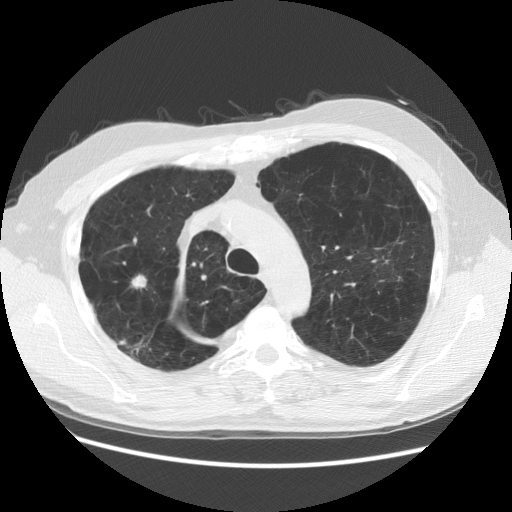
Low-dose screening chest CT, axial slice. Third annual screen. Lung window (W 1500 / L -600 HU). Slice 103 of 137 in the series. 512 × 512 image matrix. Male, age 58 years at enrolment. Former smoker at enrolment.
Expert-annotated lung lesion, bounding box [x1, y1, x2, y2] px = [113, 258, 159, 306]. The screening reader recorded 3 non-calcified nodules or masses ≥4 mm on this exam (right lower lobe, right upper lobe, right upper lobe); which of them this box marks is not recorded. Participant outcome: lung cancer diagnosed 88 days after this screen — squamous cell carcinoma, NOS, right upper lobe, moderately differentiated (G2), stage IB (AJCC 6th edition), 18 mm at pathology.